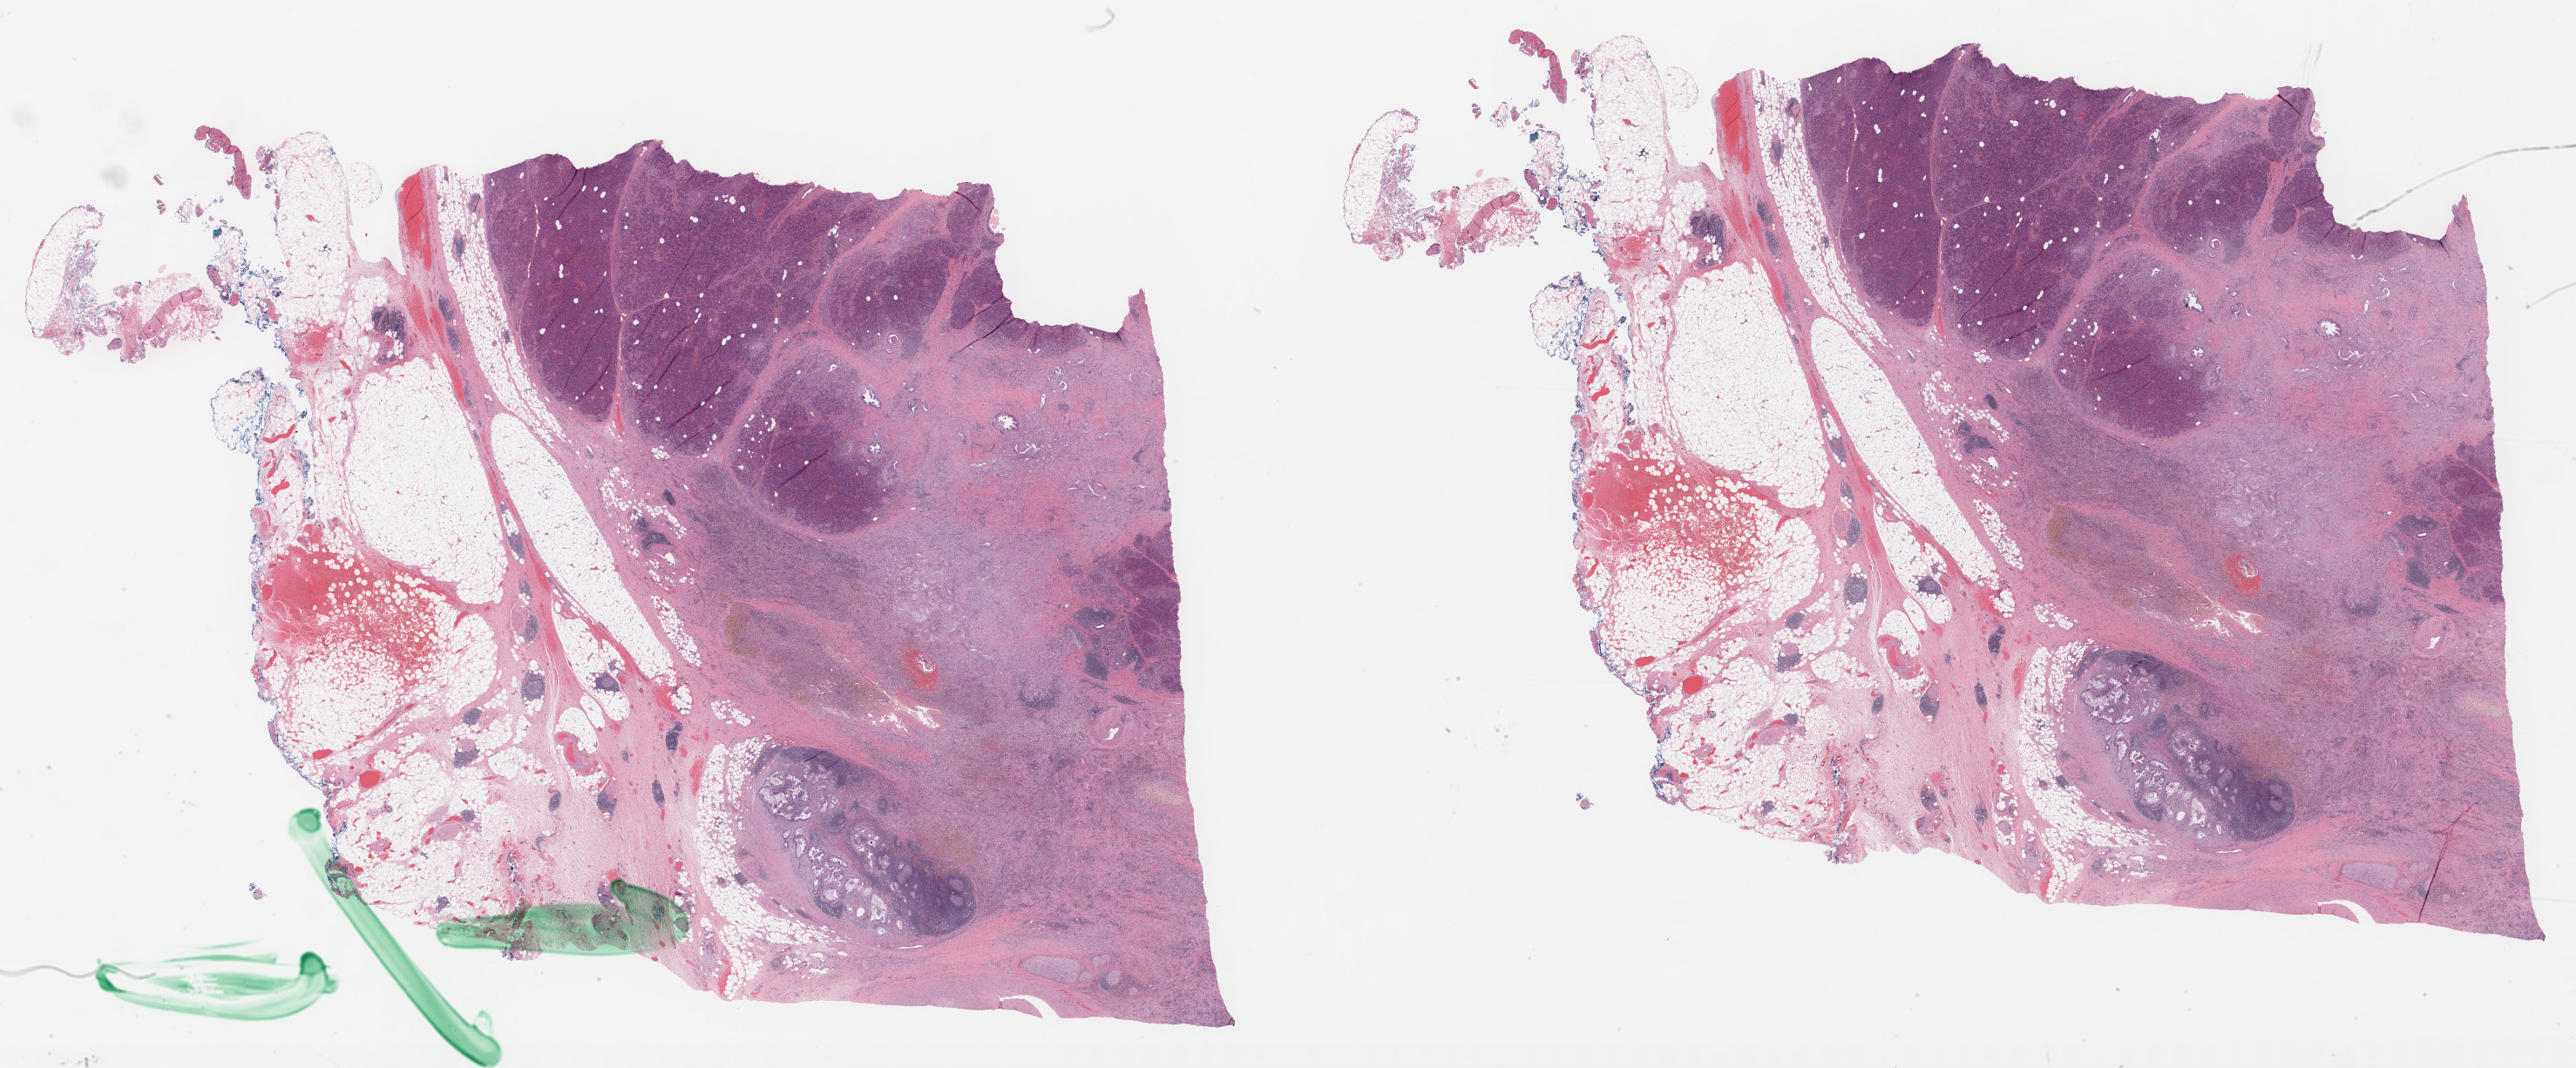
Whole-slide histology image, H&E, low-resolution overview of the scanned area, about 47.8 x 19.8 mm (from a 40x scan), formalin-fixed paraffin-embedded (FFPE) diagnostic section, pancreas, primary tumour sample. Patient: male, age at initial diagnosis 81 years.
Histologic diagnosis: Infiltrating duct carcinoma, NOS (body of pancreas).